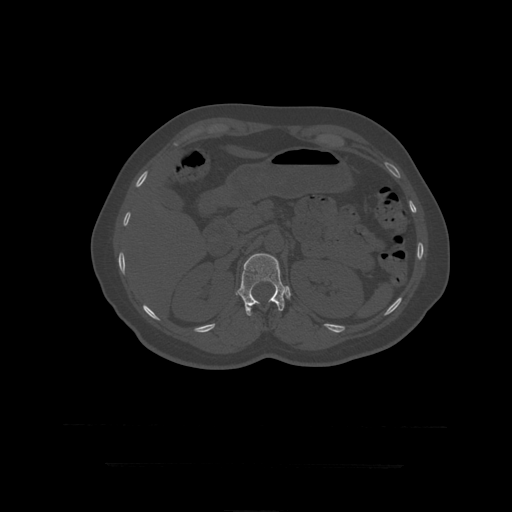
CT including the spine, one axial slice. Slice 179 of 399 in the series (ordered by position). 120 kVp. Bone window (W 1800 / L 400 HU). 1.25 mm slice thickness. 512 × 512 image matrix. Patient age 41 years. Case-level facts recorded for this patient, not image findings: primary cancer: breast.
Annotated regions visible in this slice (semi-automatically segmented with operator editing):
- L1 vertebra: bounding box (x1, y1, x2, y2) in pixels: (238, 254, 285, 316)